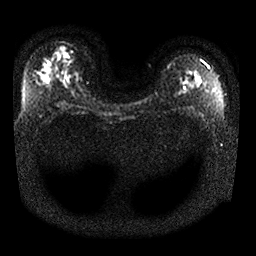
Breast MRI, one axial slice. Slice 17 of 25 in the series (ordered by position). Diffusion-weighted series; image 2 of 4 stored at this slice position (different b-values; order by instance number). 1.5 T. 4 mm slice thickness. 256 × 256 image matrix, field of view 340 × 340 mm. Female patient.
Outlined on this slice (expert manual segmentation):
- tumour on diffusion-weighted imaging: box from (x=54, y=47) to (x=69, y=58) px